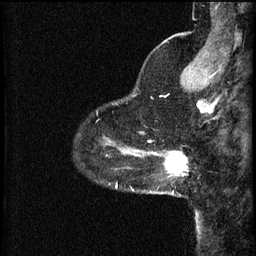
Breast MRI (dynamic contrast-enhanced), one sagittal slice; slice 11 of 60 in the series (ordered by position); 3 images stored at this slice position (order not interpretable as contrast timing); 1.5 T; TE 4.2 ms, TR 8.2 ms; 2 mm slice thickness; 256 × 256 image matrix, field of view 200 × 200 mm. Patient: female, 37 years.
Outlined on this slice (semi-automatically segmented with operator editing):
- analysis volume of interest (the breast-tissue region the enhancement analysis was run in; not a lesion): bounding box (x1, y1, x2, y2) in pixels: (148, 150, 189, 195)
- tumour enhancement mask (voxels above the 70 % enhancement threshold inside the analysis volume of interest): (154, 152, 189, 175)